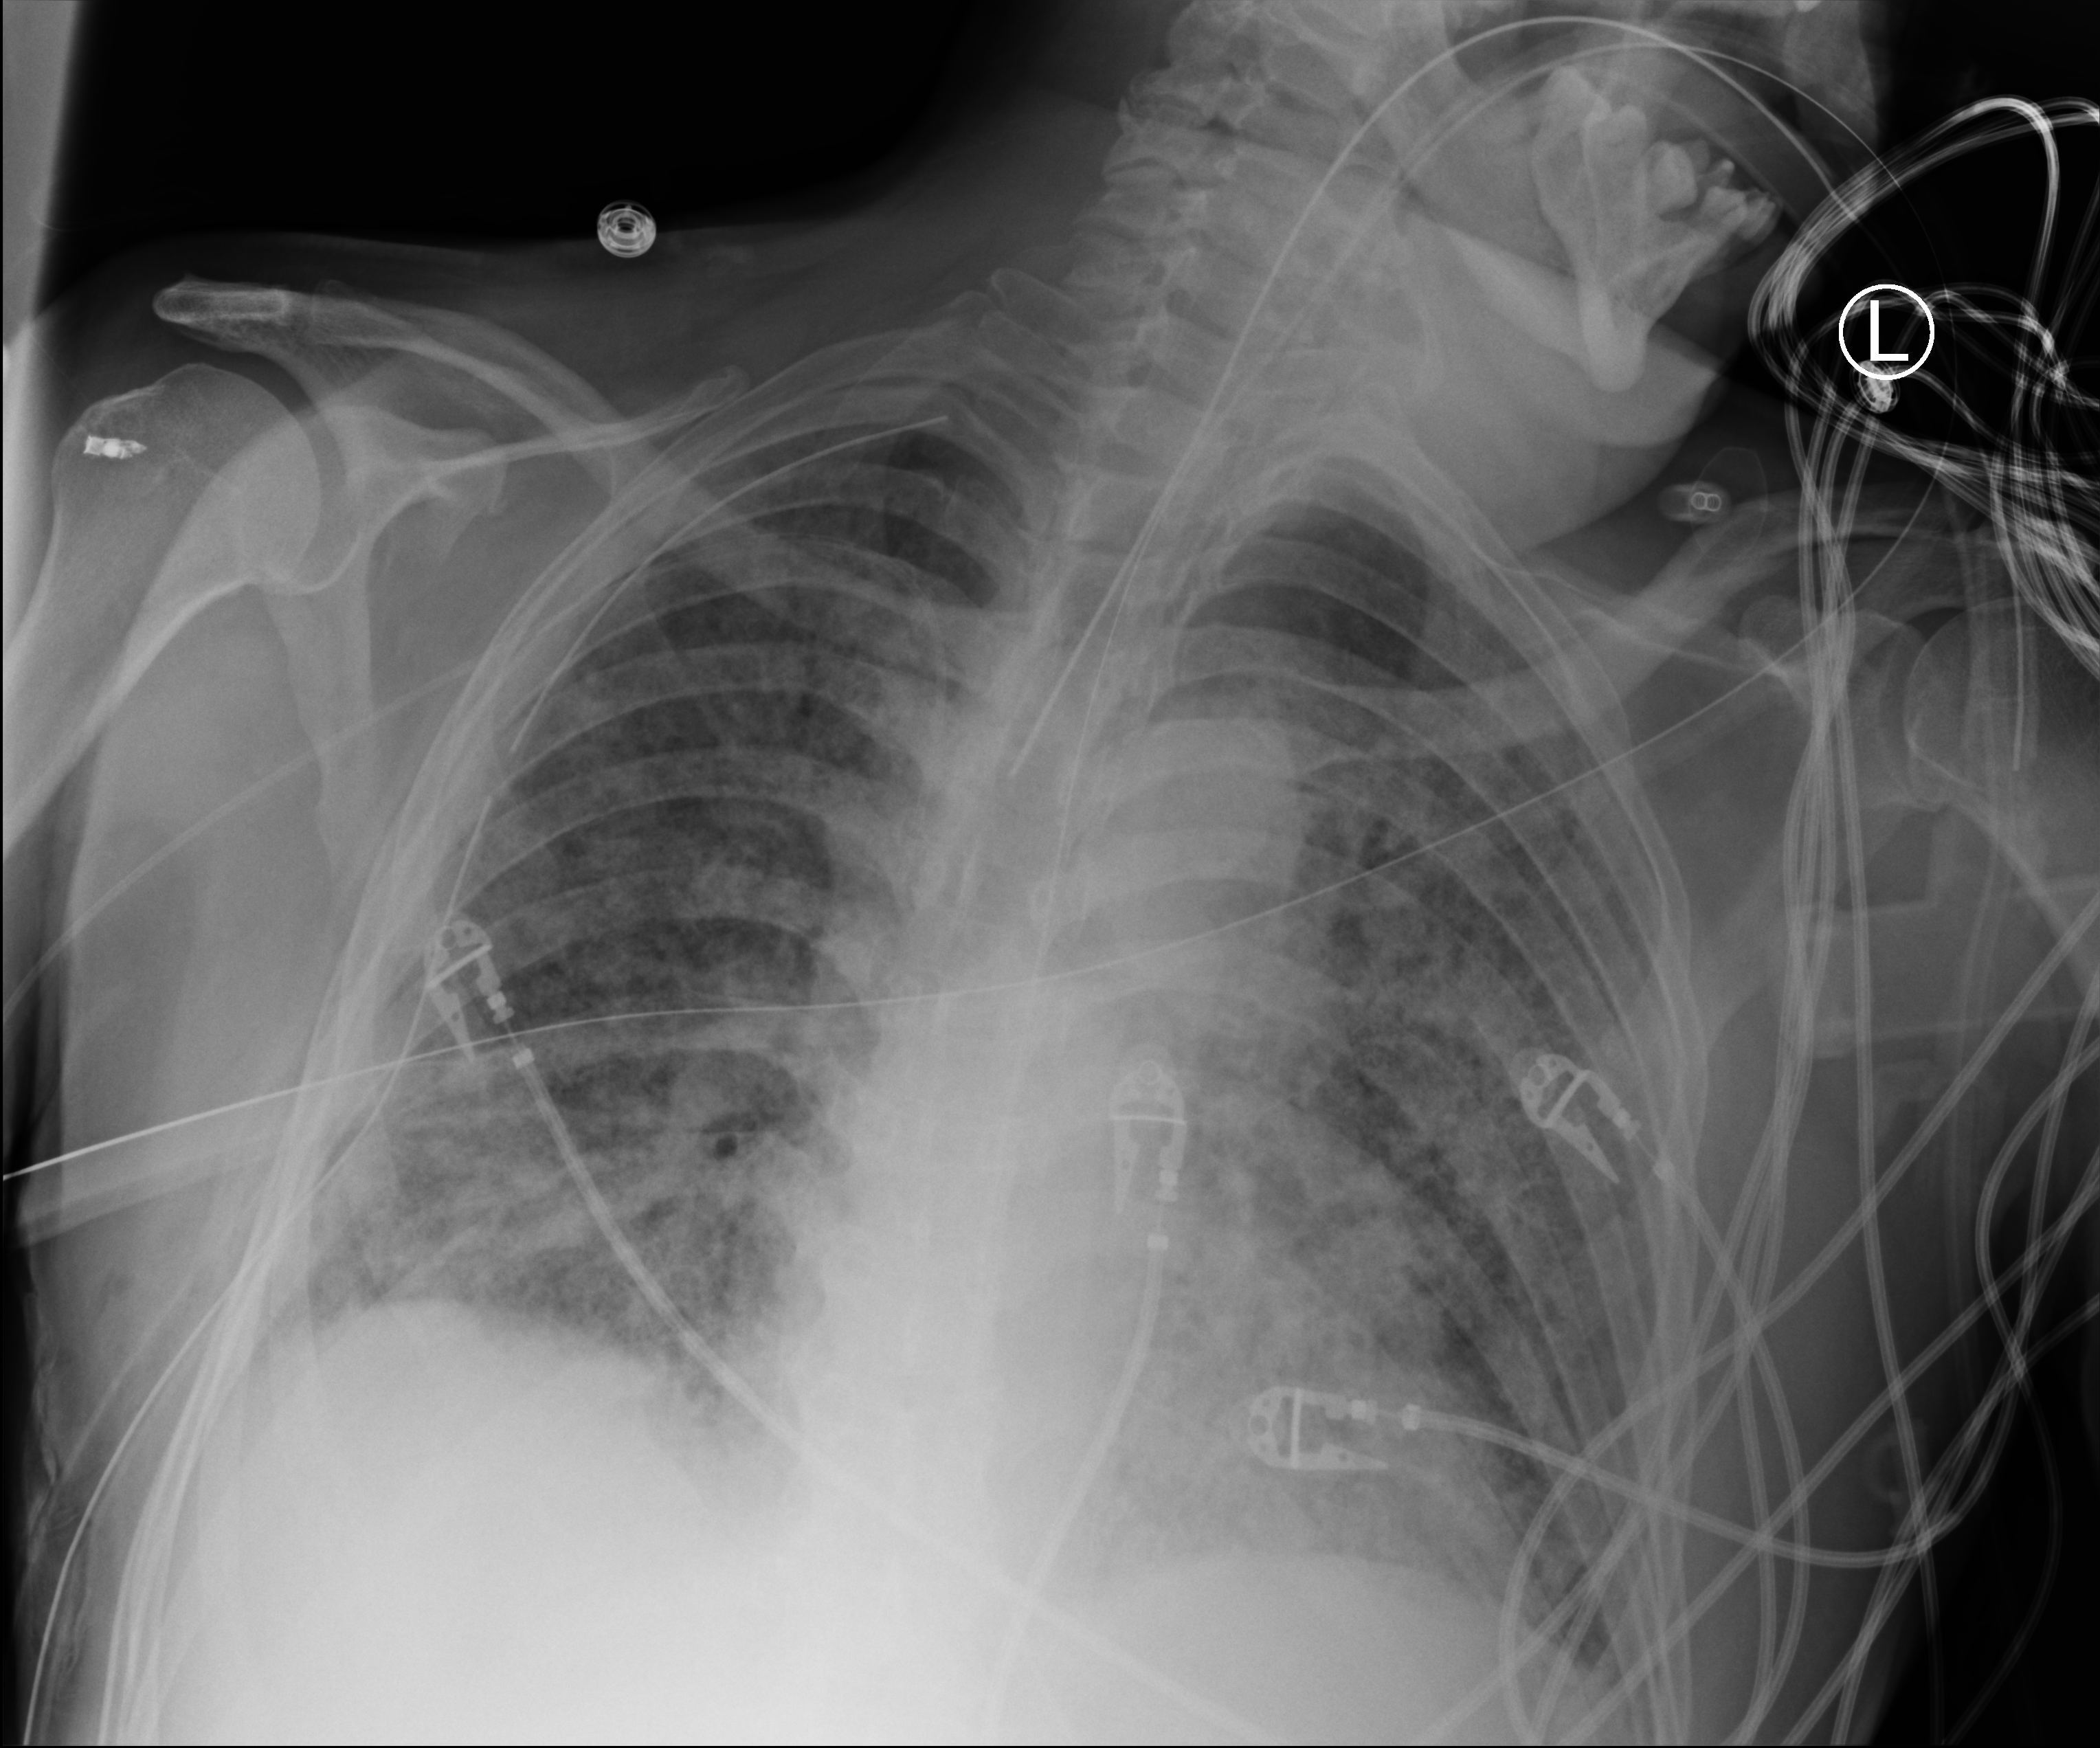
Chest X-ray (portable), anteroposterior (AP) projection. Male patient hospitalised with COVID-19, age 60–74 years.
Hospital-stay facts (about this admission, not read from this image; timing relative to this image not recorded): mechanically ventilated during this hospital stay: yes.